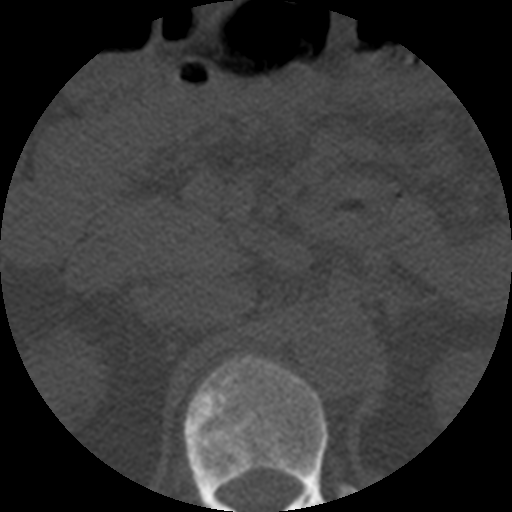
CT including the spine, one axial slice. Position 209 of 508 along the scan axis. Reconstruction kernel STANDARD. 120 kVp. Bone window (W 1800 / L 400 HU). 512 × 512 image matrix, field of view 160 × 160 mm. Patient age 57 years. From the clinical record (not read from this slice): primary cancer: prostate.
Outlined on this slice (semi-automatic segmentation, software-assisted and operator-edited):
- T12 vertebra: bounding box <183,355,328,512> (left, top, right, bottom; pixels)